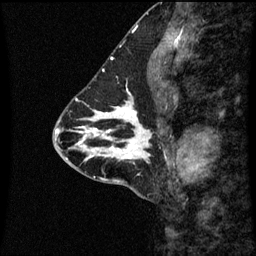
Breast MRI (dynamic contrast-enhanced), one sagittal slice. Position 26 of 60 along the scan axis. Dynamic contrast-enhanced series, image 2 of 3 at this slice position (ordered by acquisition). 1.5 T. TE 4.2 ms, TR 8.9 ms. 256 × 256 image matrix. Patient: female, 43 years. Case-level facts recorded for this patient, not image findings: setting: breast cancer imaged before/during neoadjuvant chemotherapy; receptor status: HR-positive, HER2-negative.
Annotated regions visible in this slice (semi-automatically segmented with operator editing):
- analysis volume of interest (the breast-tissue region the enhancement analysis was run in; not a lesion): bounding box <110,100,169,163> (left, top, right, bottom; pixels)
- tumour enhancement mask (voxels above the 70 % enhancement threshold inside the analysis volume of interest): <110,102,150,159>